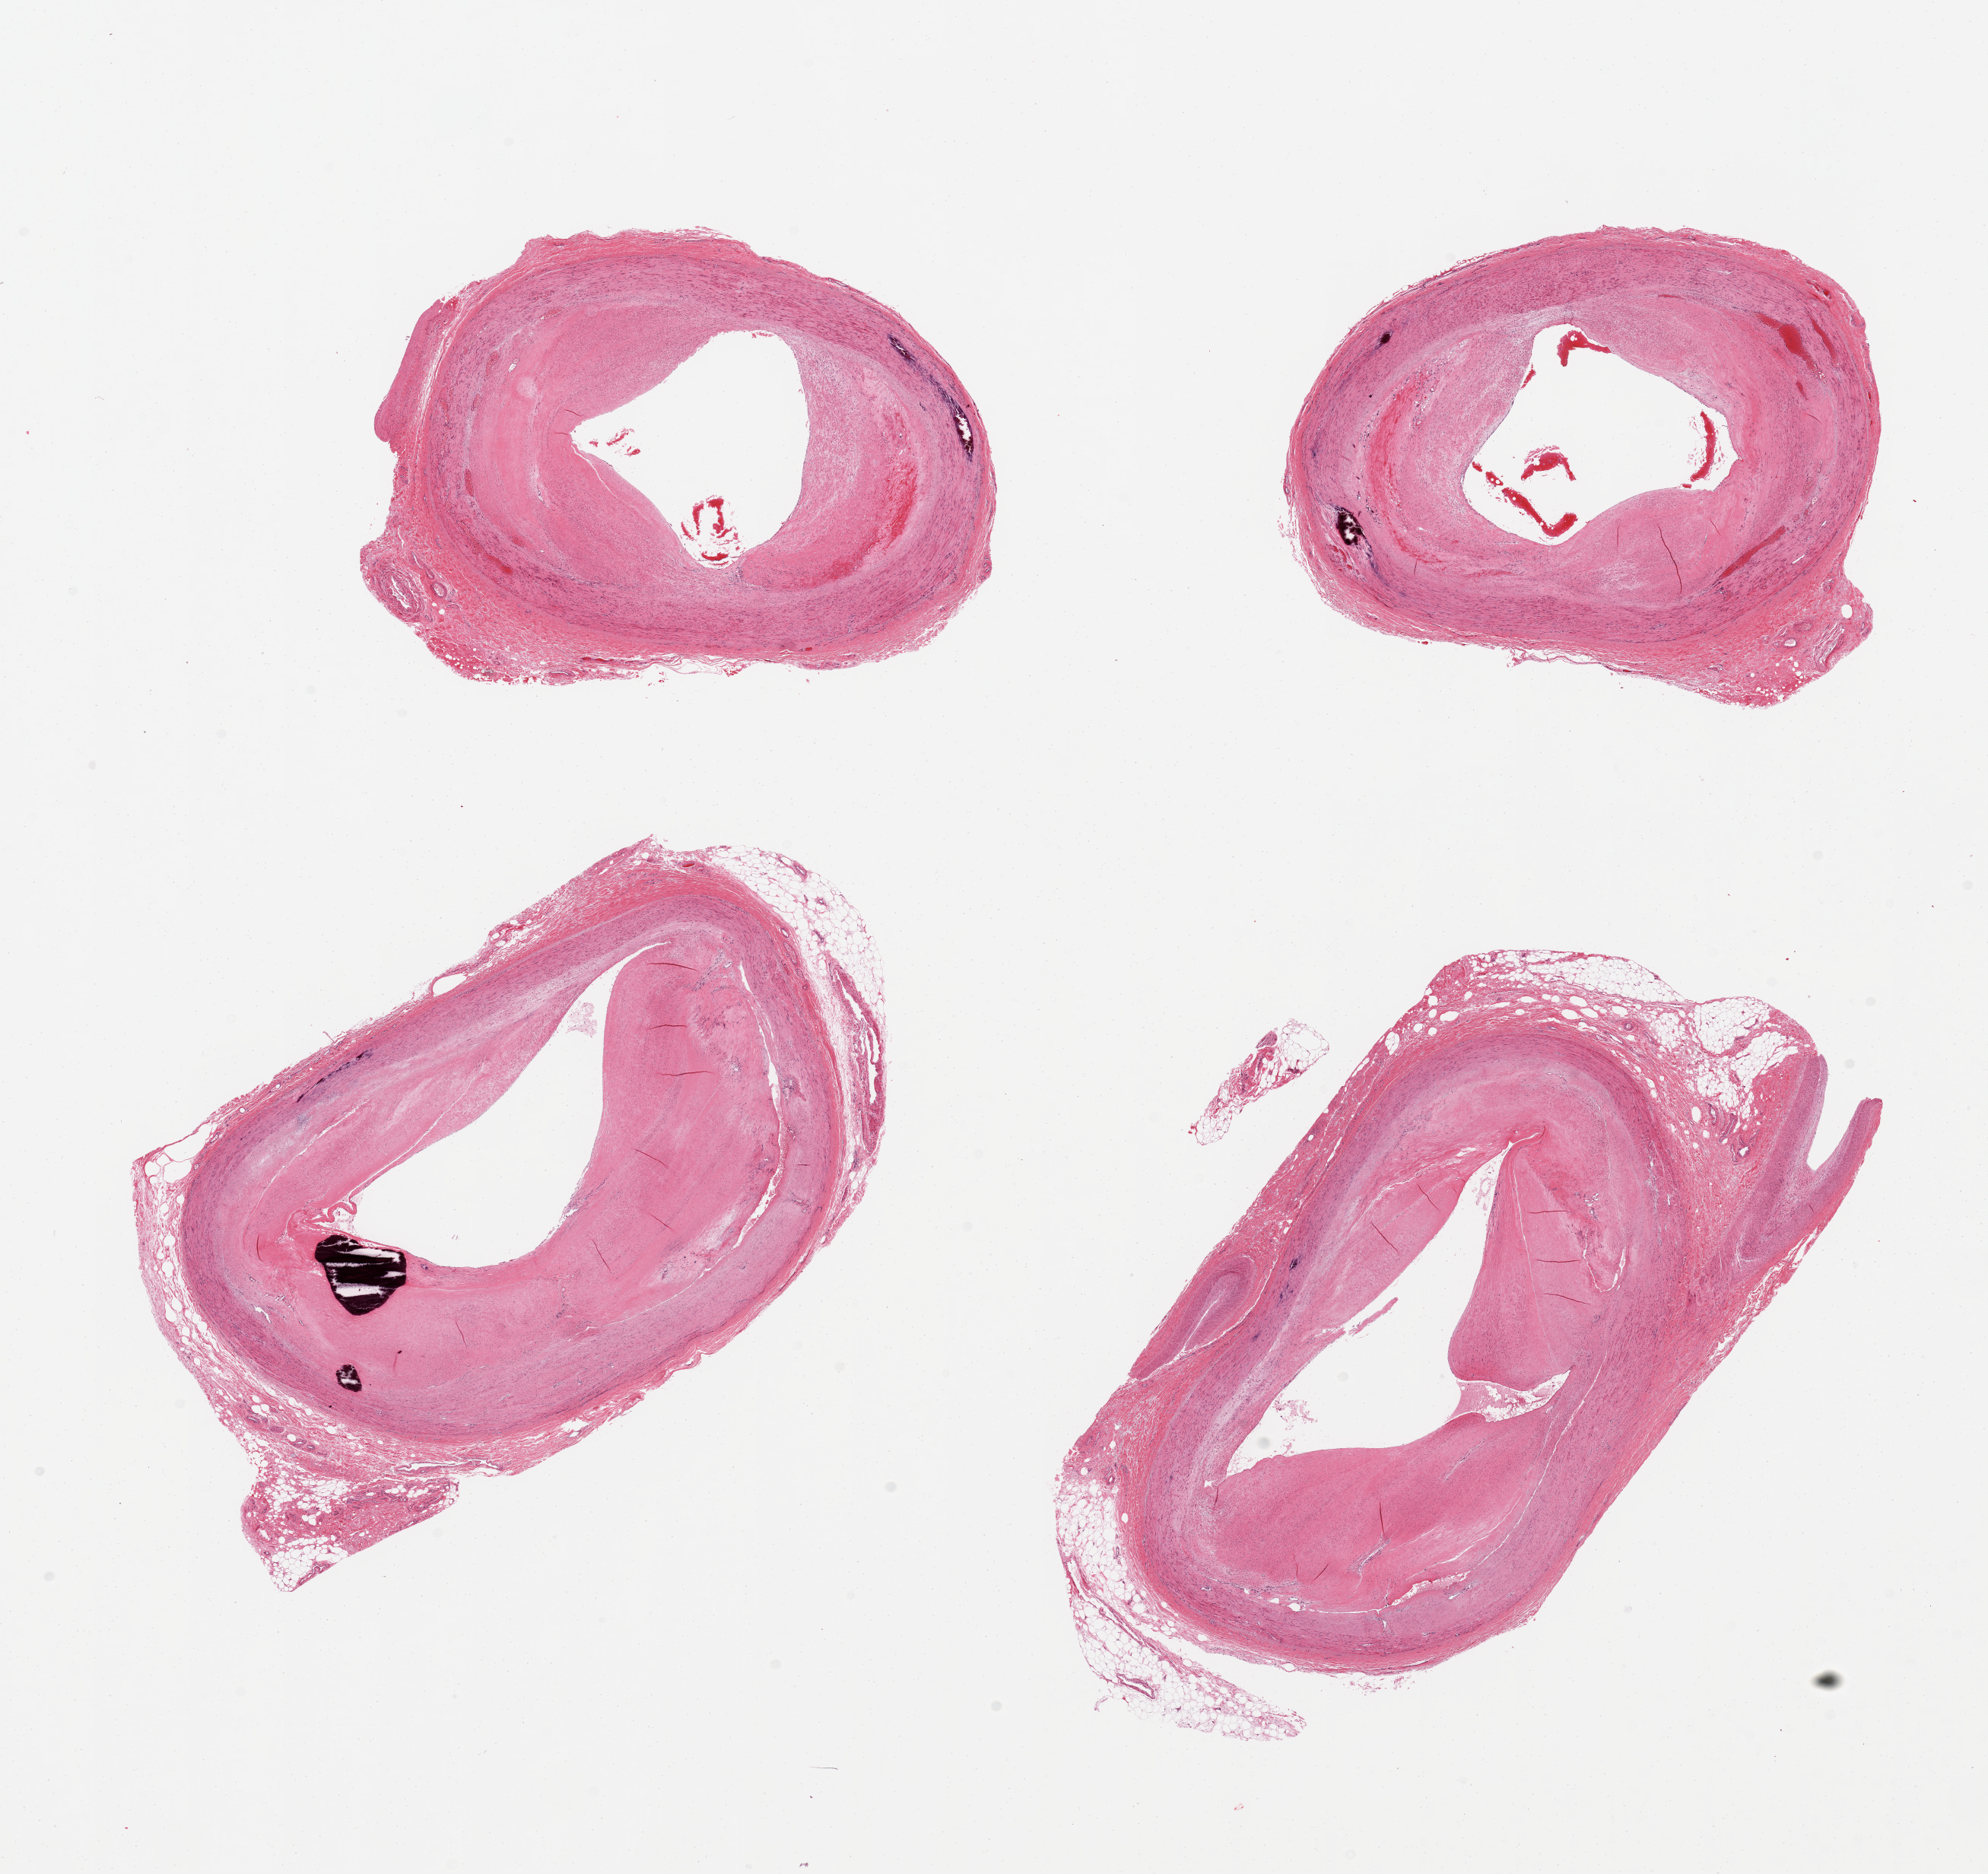
Digitized H&E-stained section, brightfield — shown as a low-resolution overview of the whole scanned area (about 20.7 x 19.5 mm, from a 20x scan); PAXgene-fixed paraffin-embedded (PFPE) section; sampled site (target tissue): tibial artery; tissue donor sample. Male donor.
Review note (as recorded): 4 pieces; patent but atherosclerotic; focal calcium.